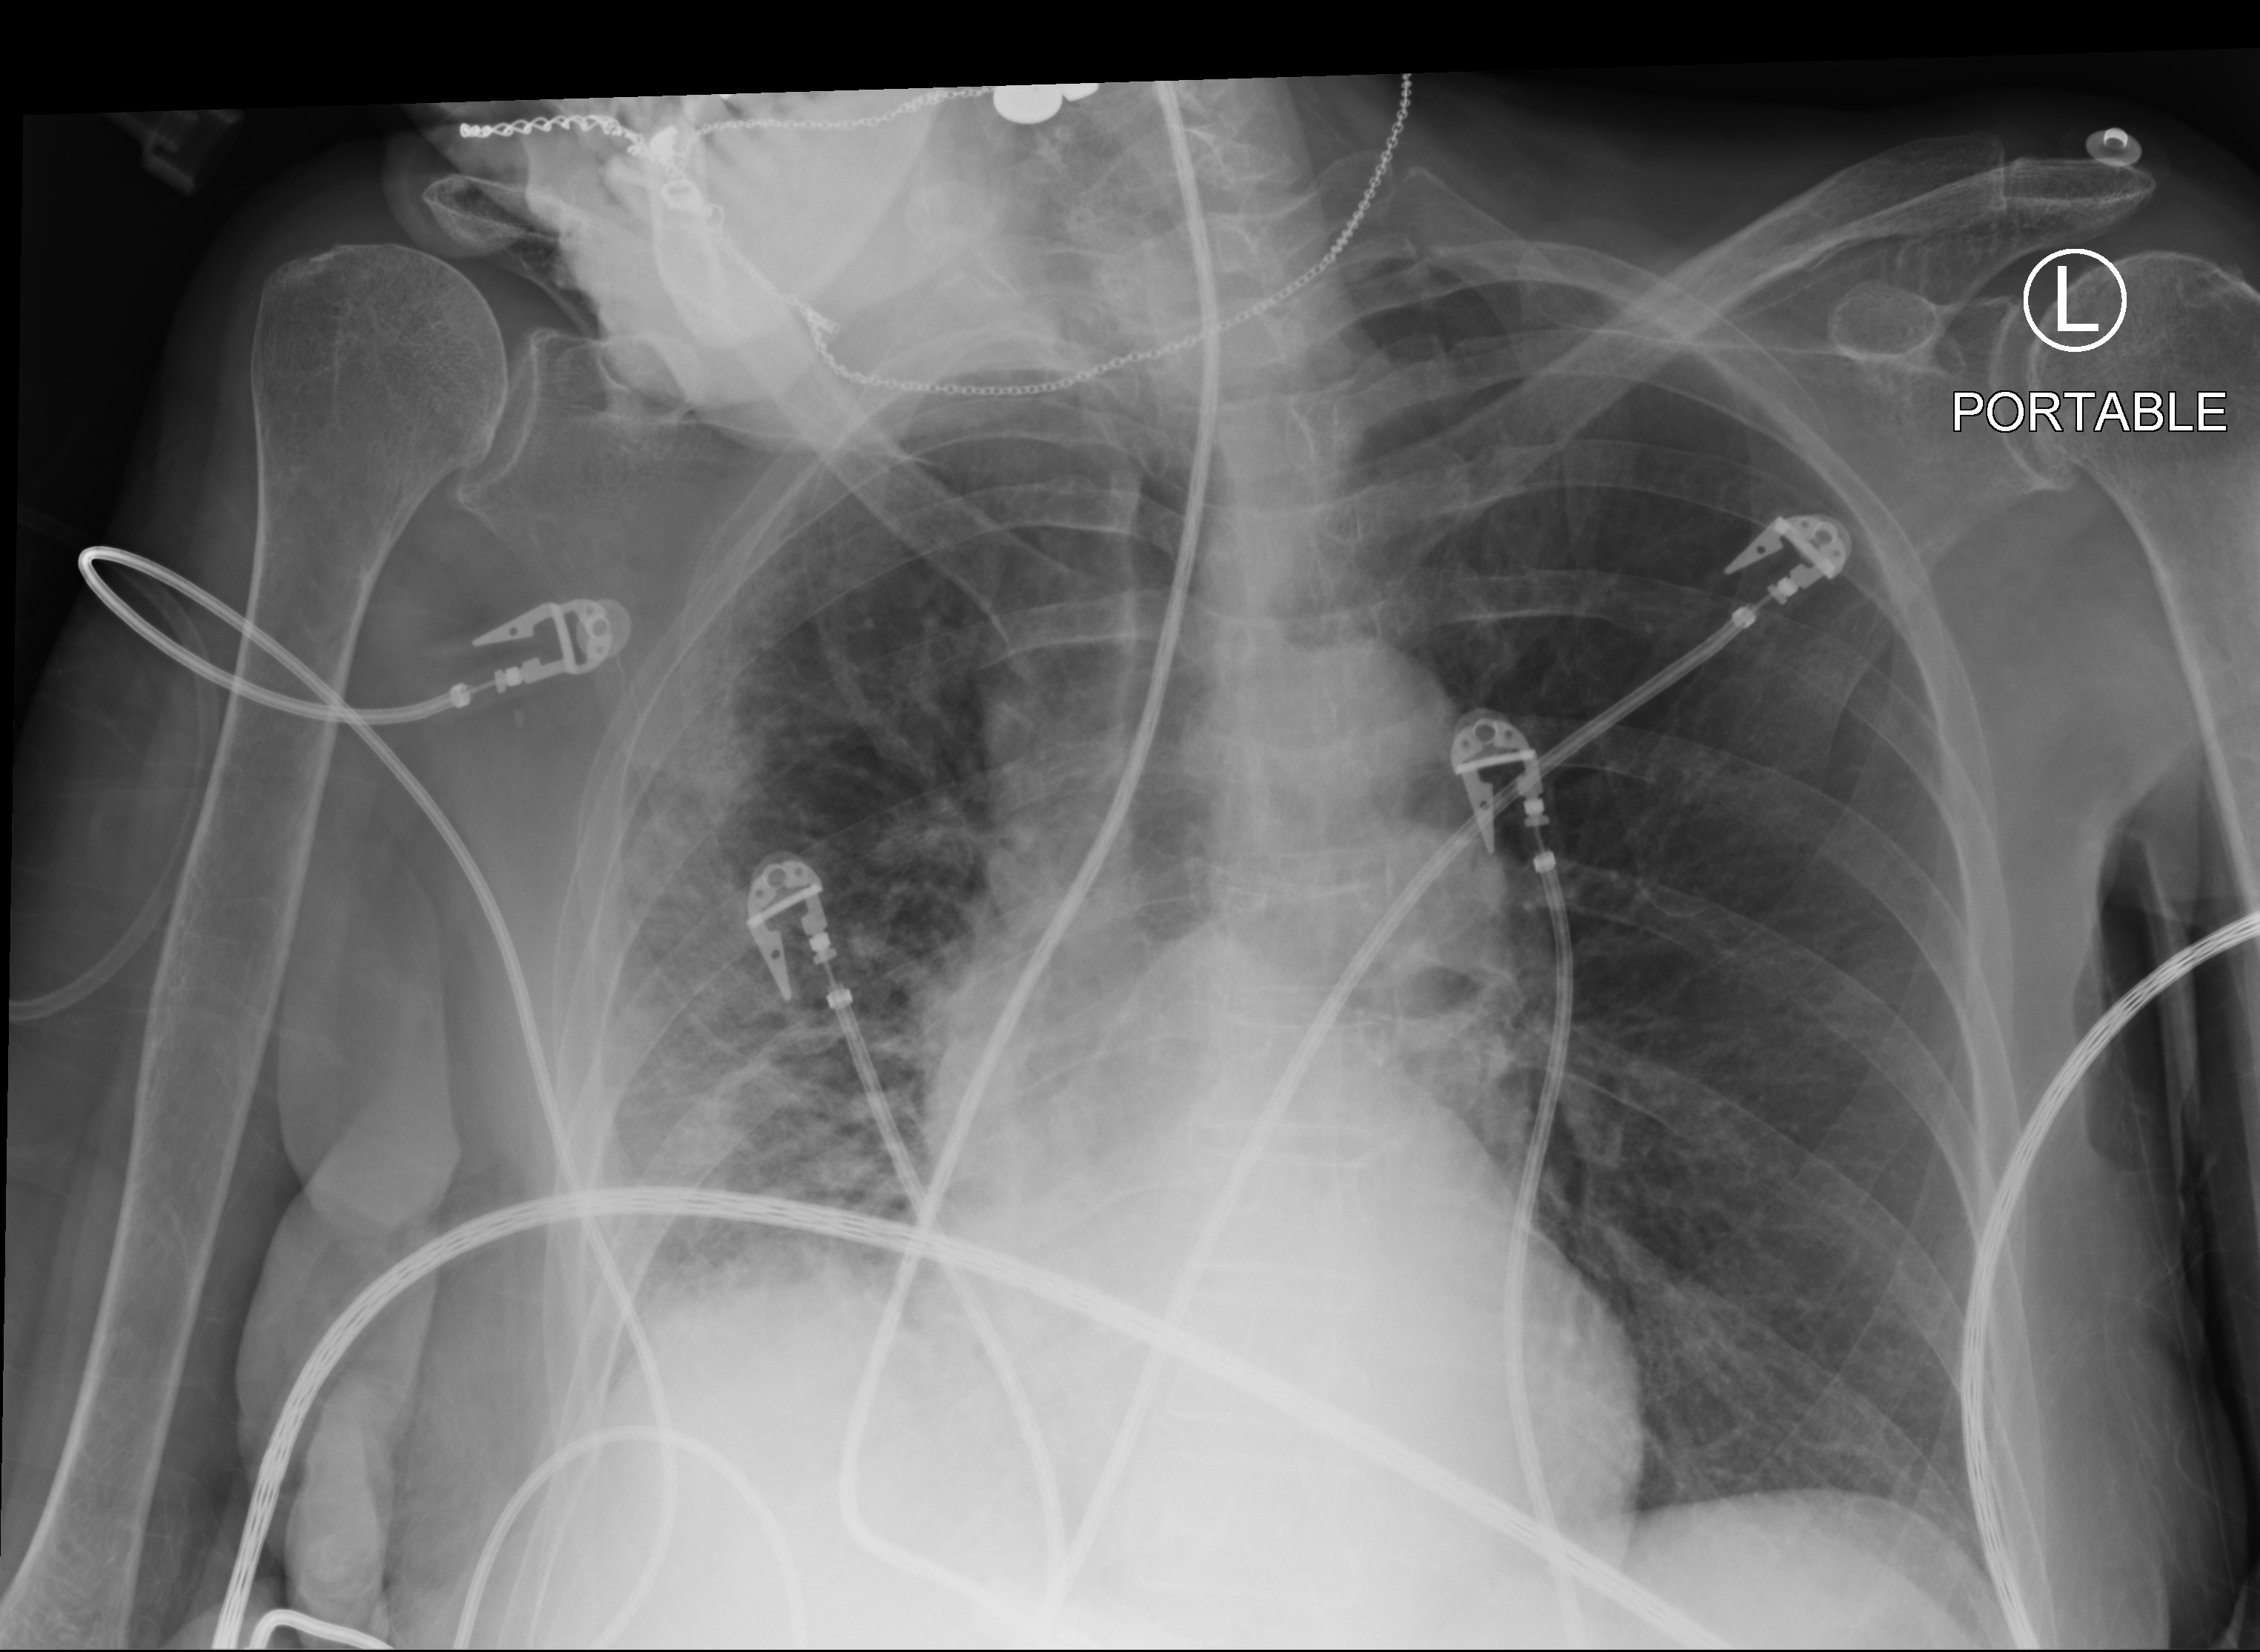
Chest X-ray (portable); anteroposterior (AP) projection. Female patient hospitalised with COVID-19, age 75–90 years.
Hospital-stay facts (about this admission, not read from this image; timing relative to this image not recorded):
- hypertension (admission record): no